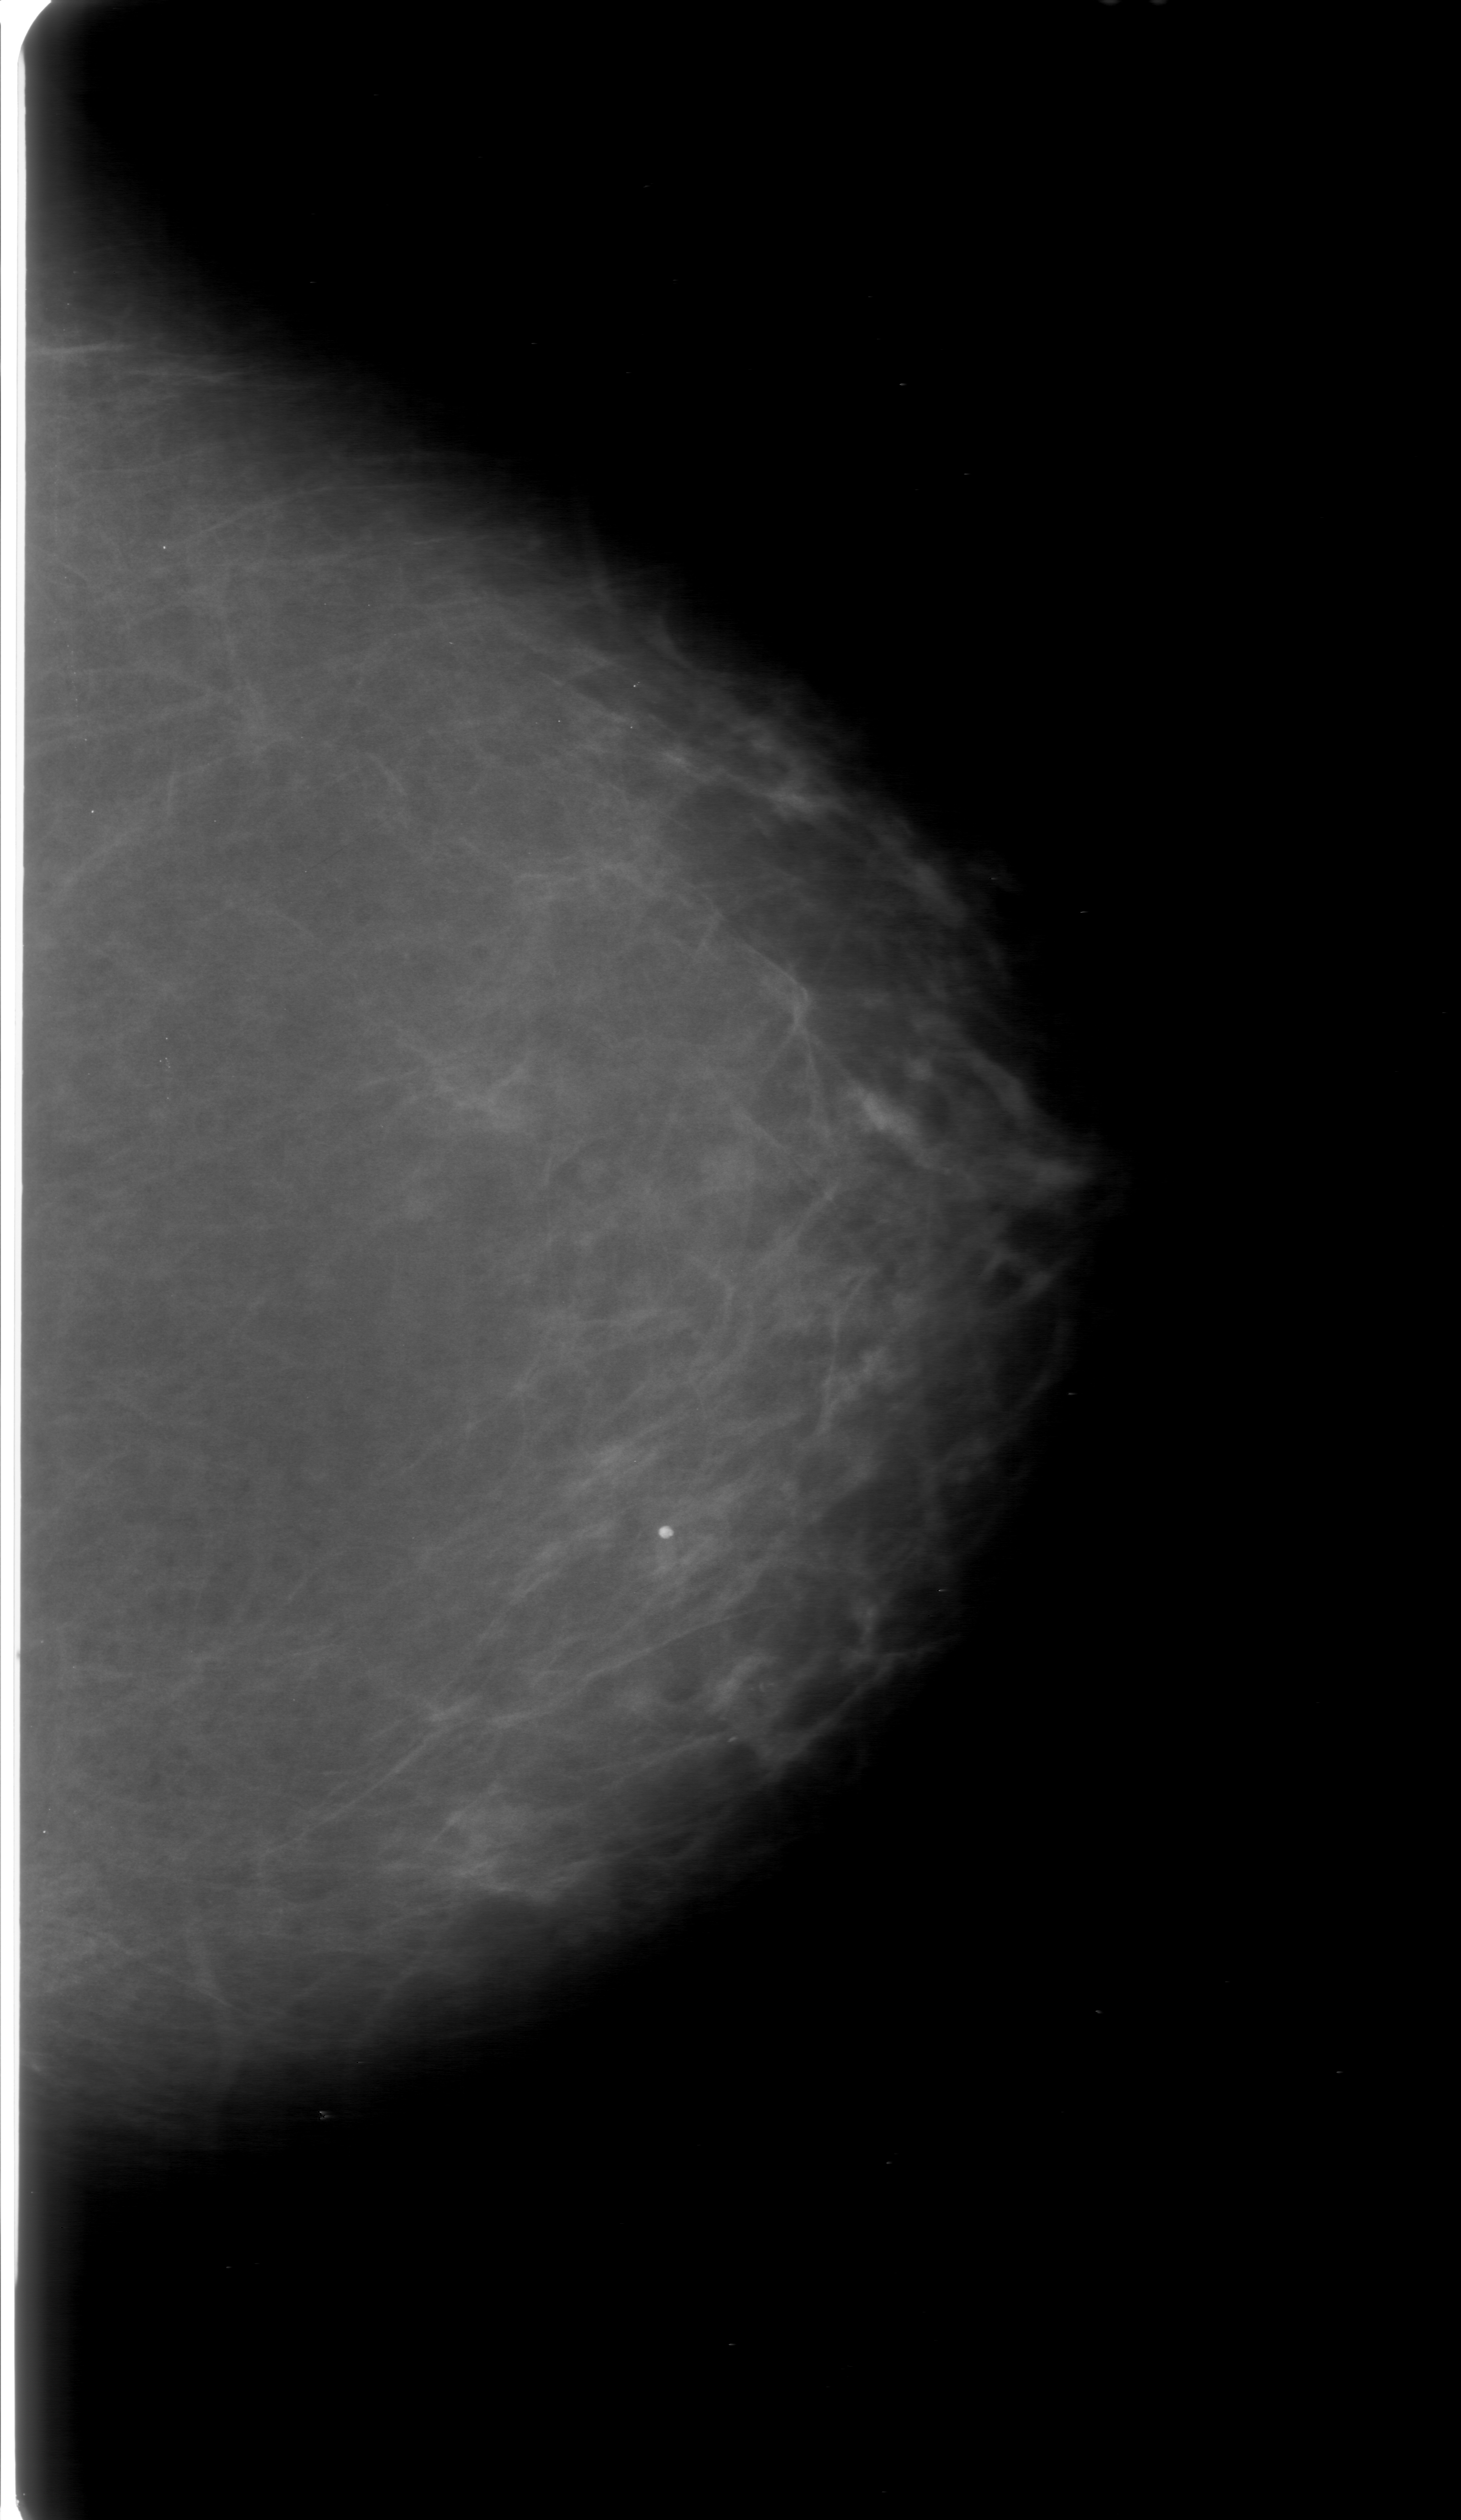
Mammogram (digitized film). Left breast. CC view. Breast composition: almost entirely fatty (BI-RADS density category 1 of 4). 1461 × 2520 image matrix.
Expert-marked regions of interest on this image (one box per marked abnormality):
- calcifications, morphology fine linear branching, distribution clustered; BI-RADS assessment category 3; subtlety rating 2 on a 1 (subtle) to 5 (obvious) scale; pathology result (as recorded, not read from the image): malignant: box from (x=581, y=1543) to (x=903, y=1853) px